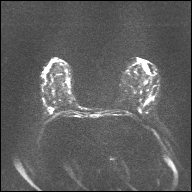
Breast MRI, one axial slice; position 16 of 32 along the scan axis; diffusion-weighted series; image 2 of 4 stored at this slice position (different b-values; order by instance number); 1.5 T; 4 mm slice thickness; 192 × 192 image matrix, field of view 360 × 360 mm. Female patient.
Annotated regions visible in this slice (manually delineated by an expert):
- tumour on diffusion-weighted imaging: box from (x=47, y=108) to (x=54, y=112) px